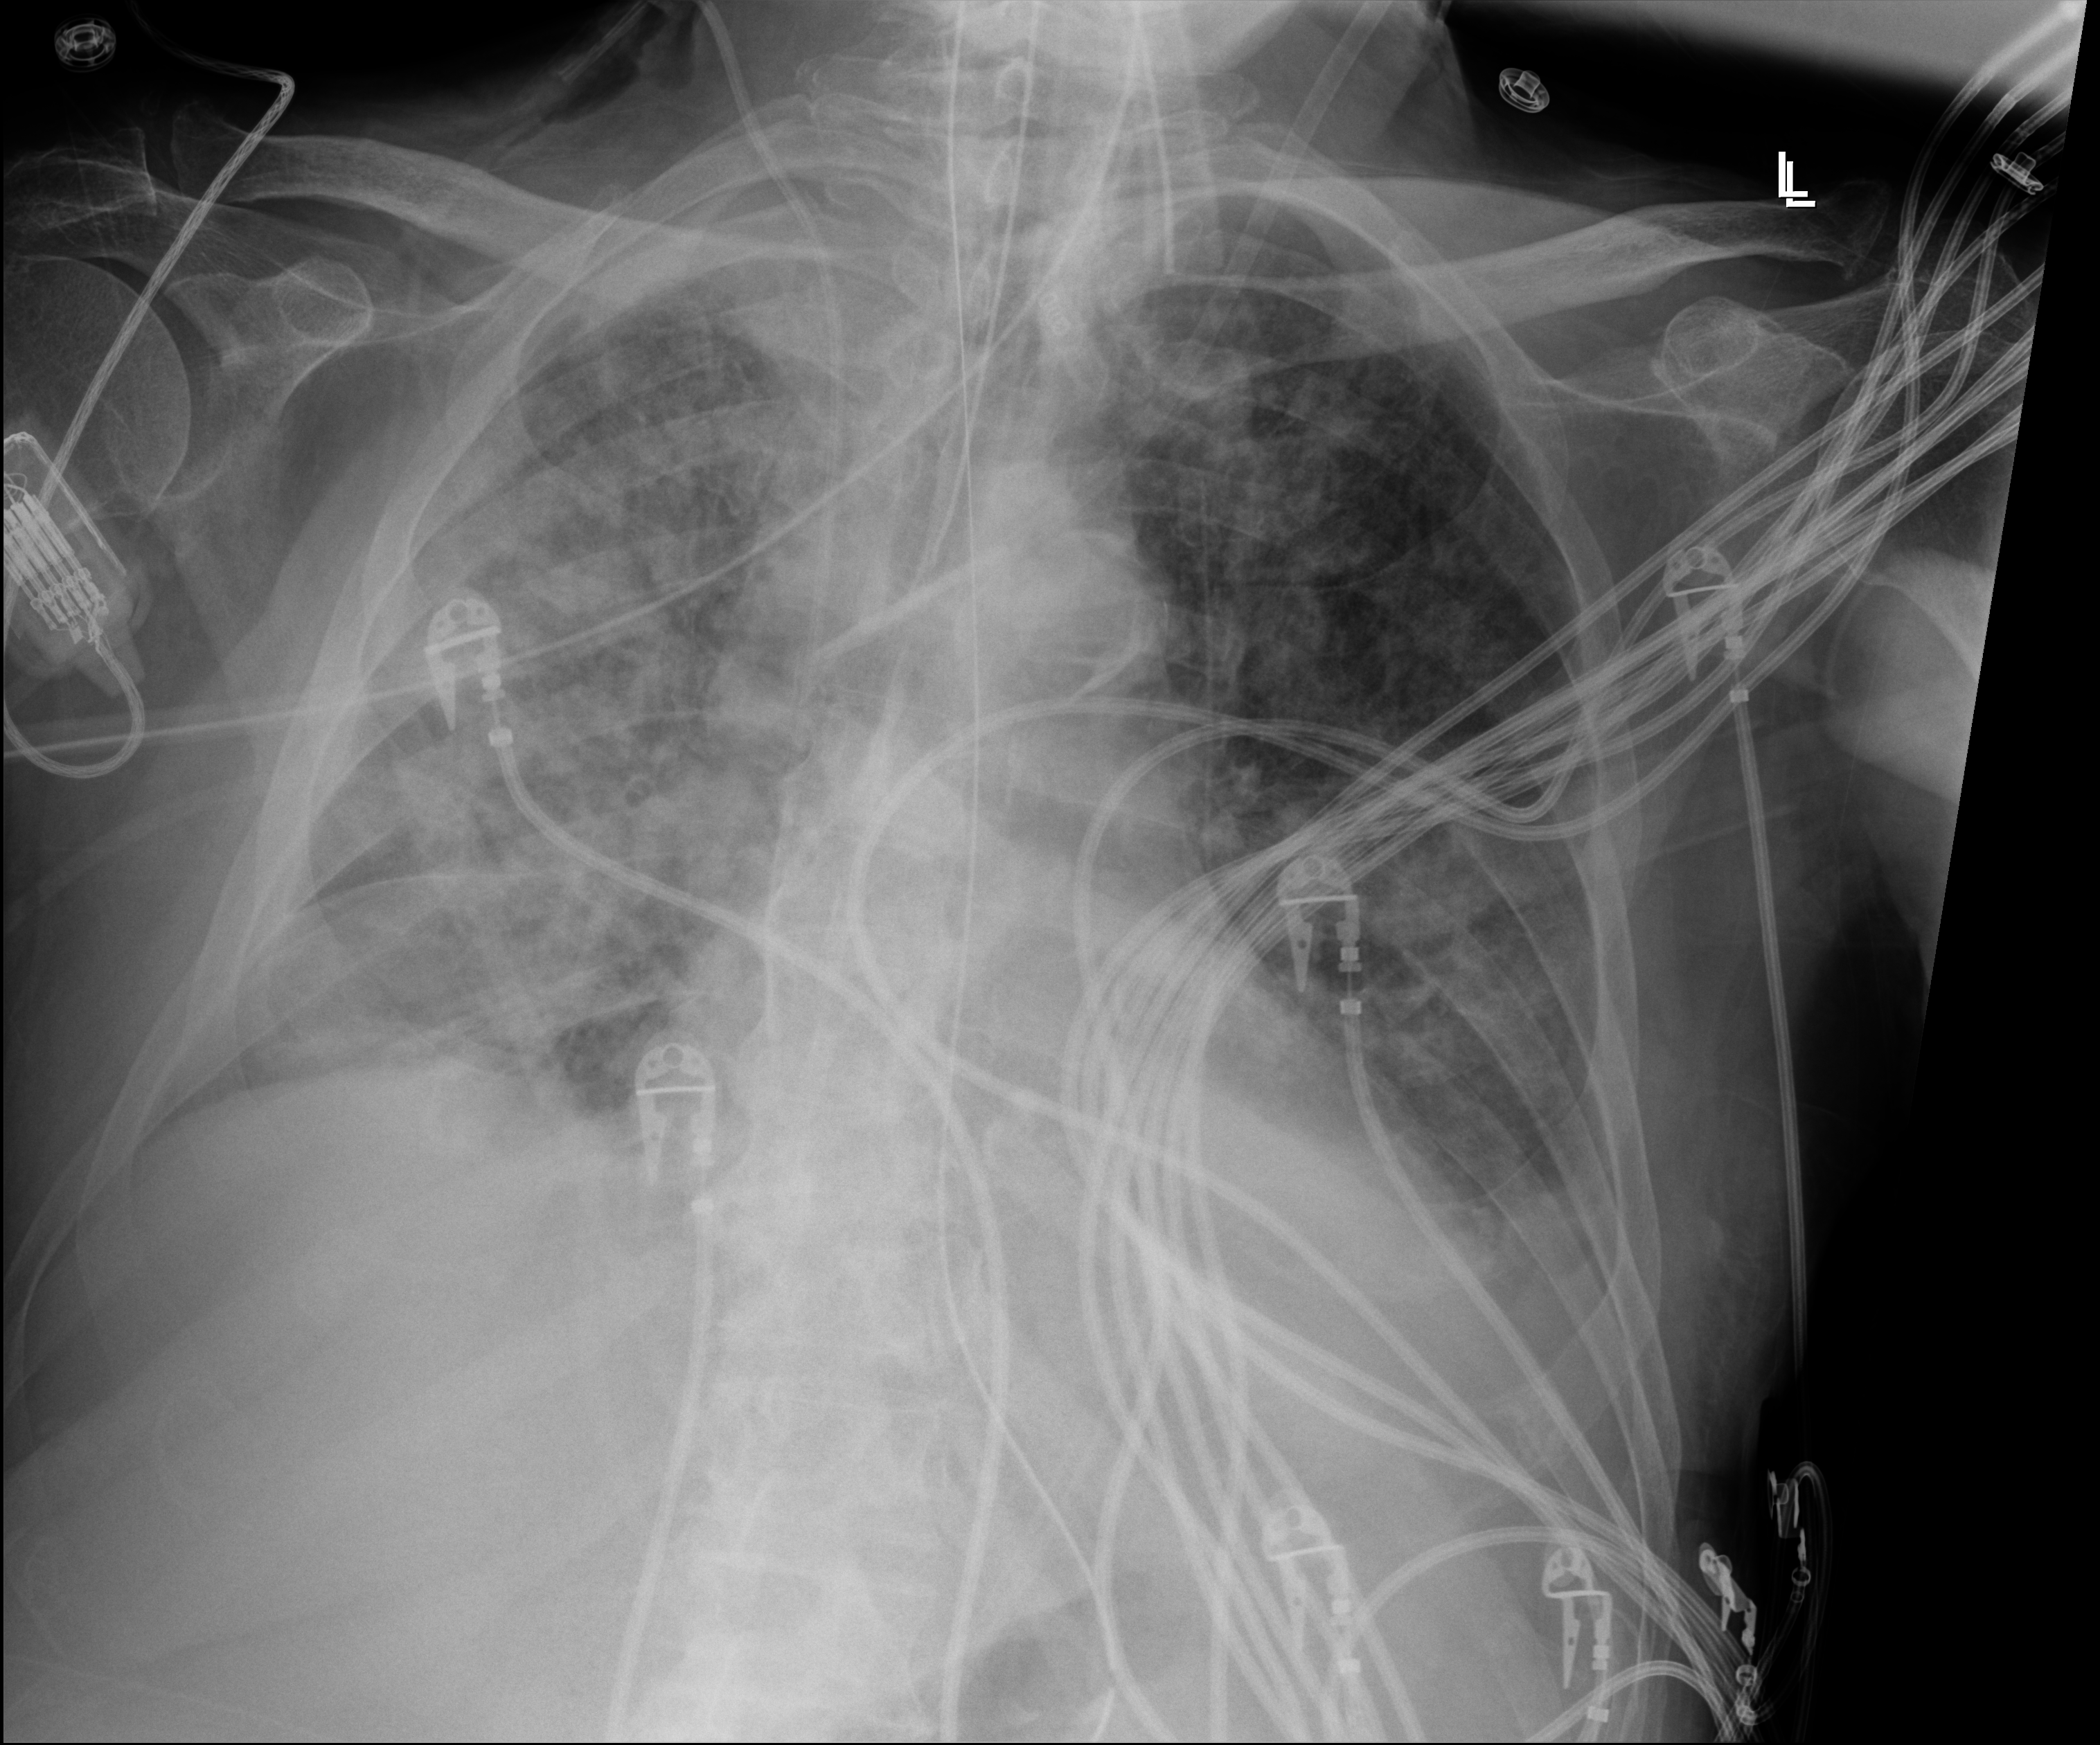
Portable chest radiograph, anteroposterior (AP) projection. Patient hospitalised with COVID-19; male, aged 75–90 years.
From the hospital-stay record, not from the radiograph (when in the stay this image was taken is not recorded): chronic kidney disease (admission record): no; admitted to intensive care during this hospital stay: yes; other chronic lung disease (admission record): no.